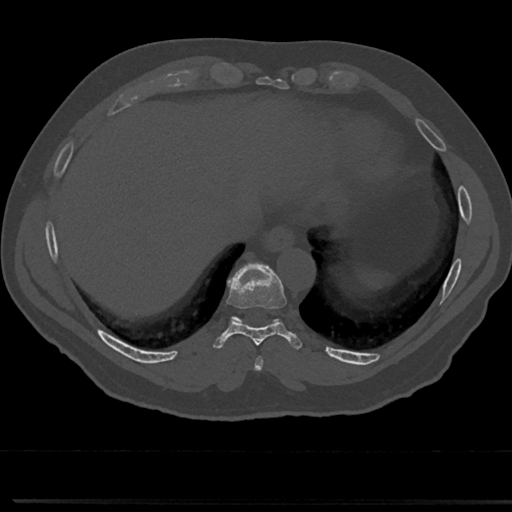
CT including the spine, one axial slice; position 298 of 817 along the scan axis; 120 kVp; bone window (W 1800 / L 400 HU); 0.5 mm slice thickness; 512 × 512 image matrix, field of view 355 × 355 mm. Male patient, age 61 years. From the clinical record (not read from this slice): primary cancer: prostate.
Annotated regions visible in this slice (semi-automatic segmentation, software-assisted and operator-edited):
- T8 vertebra: bounding box <236,326,283,357> (left, top, right, bottom; pixels)
- T9 vertebra: <232,266,283,330>